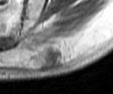
MRI of an extremity soft-tissue mass, one axial slice. Slice 12 of 42 in the series (ordered by position). MR volume resampled by the dataset authors to the PET/CT grid (not the native acquisition matrix). 3.27 mm slice thickness. 113 × 94 image matrix, field of view 110 × 92 mm. Male patient. Case-level facts recorded for this patient, not image findings: histological type: leiomyosarcoma; grade: intermediate; site of the primary tumour: left pelvis.
Annotated regions visible in this slice (expert contour drawn on MRI and transferred to this co-registered scan by the dataset authors):
- gross tumour volume (mass): bounding box (x1, y1, x2, y2) in pixels: (47, 50, 64, 63)